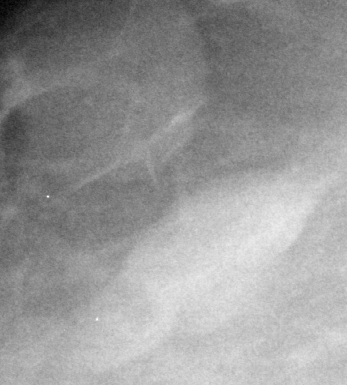
Region of interest cut from a scanned film mammogram (one marked finding), right breast, MLO view.
Marked abnormality: mass, shape round, margins circumscribed; BI-RADS assessment category 2; subtlety rating 5 on a 1 (subtle) to 5 (obvious) scale; pathology (as recorded): benign.